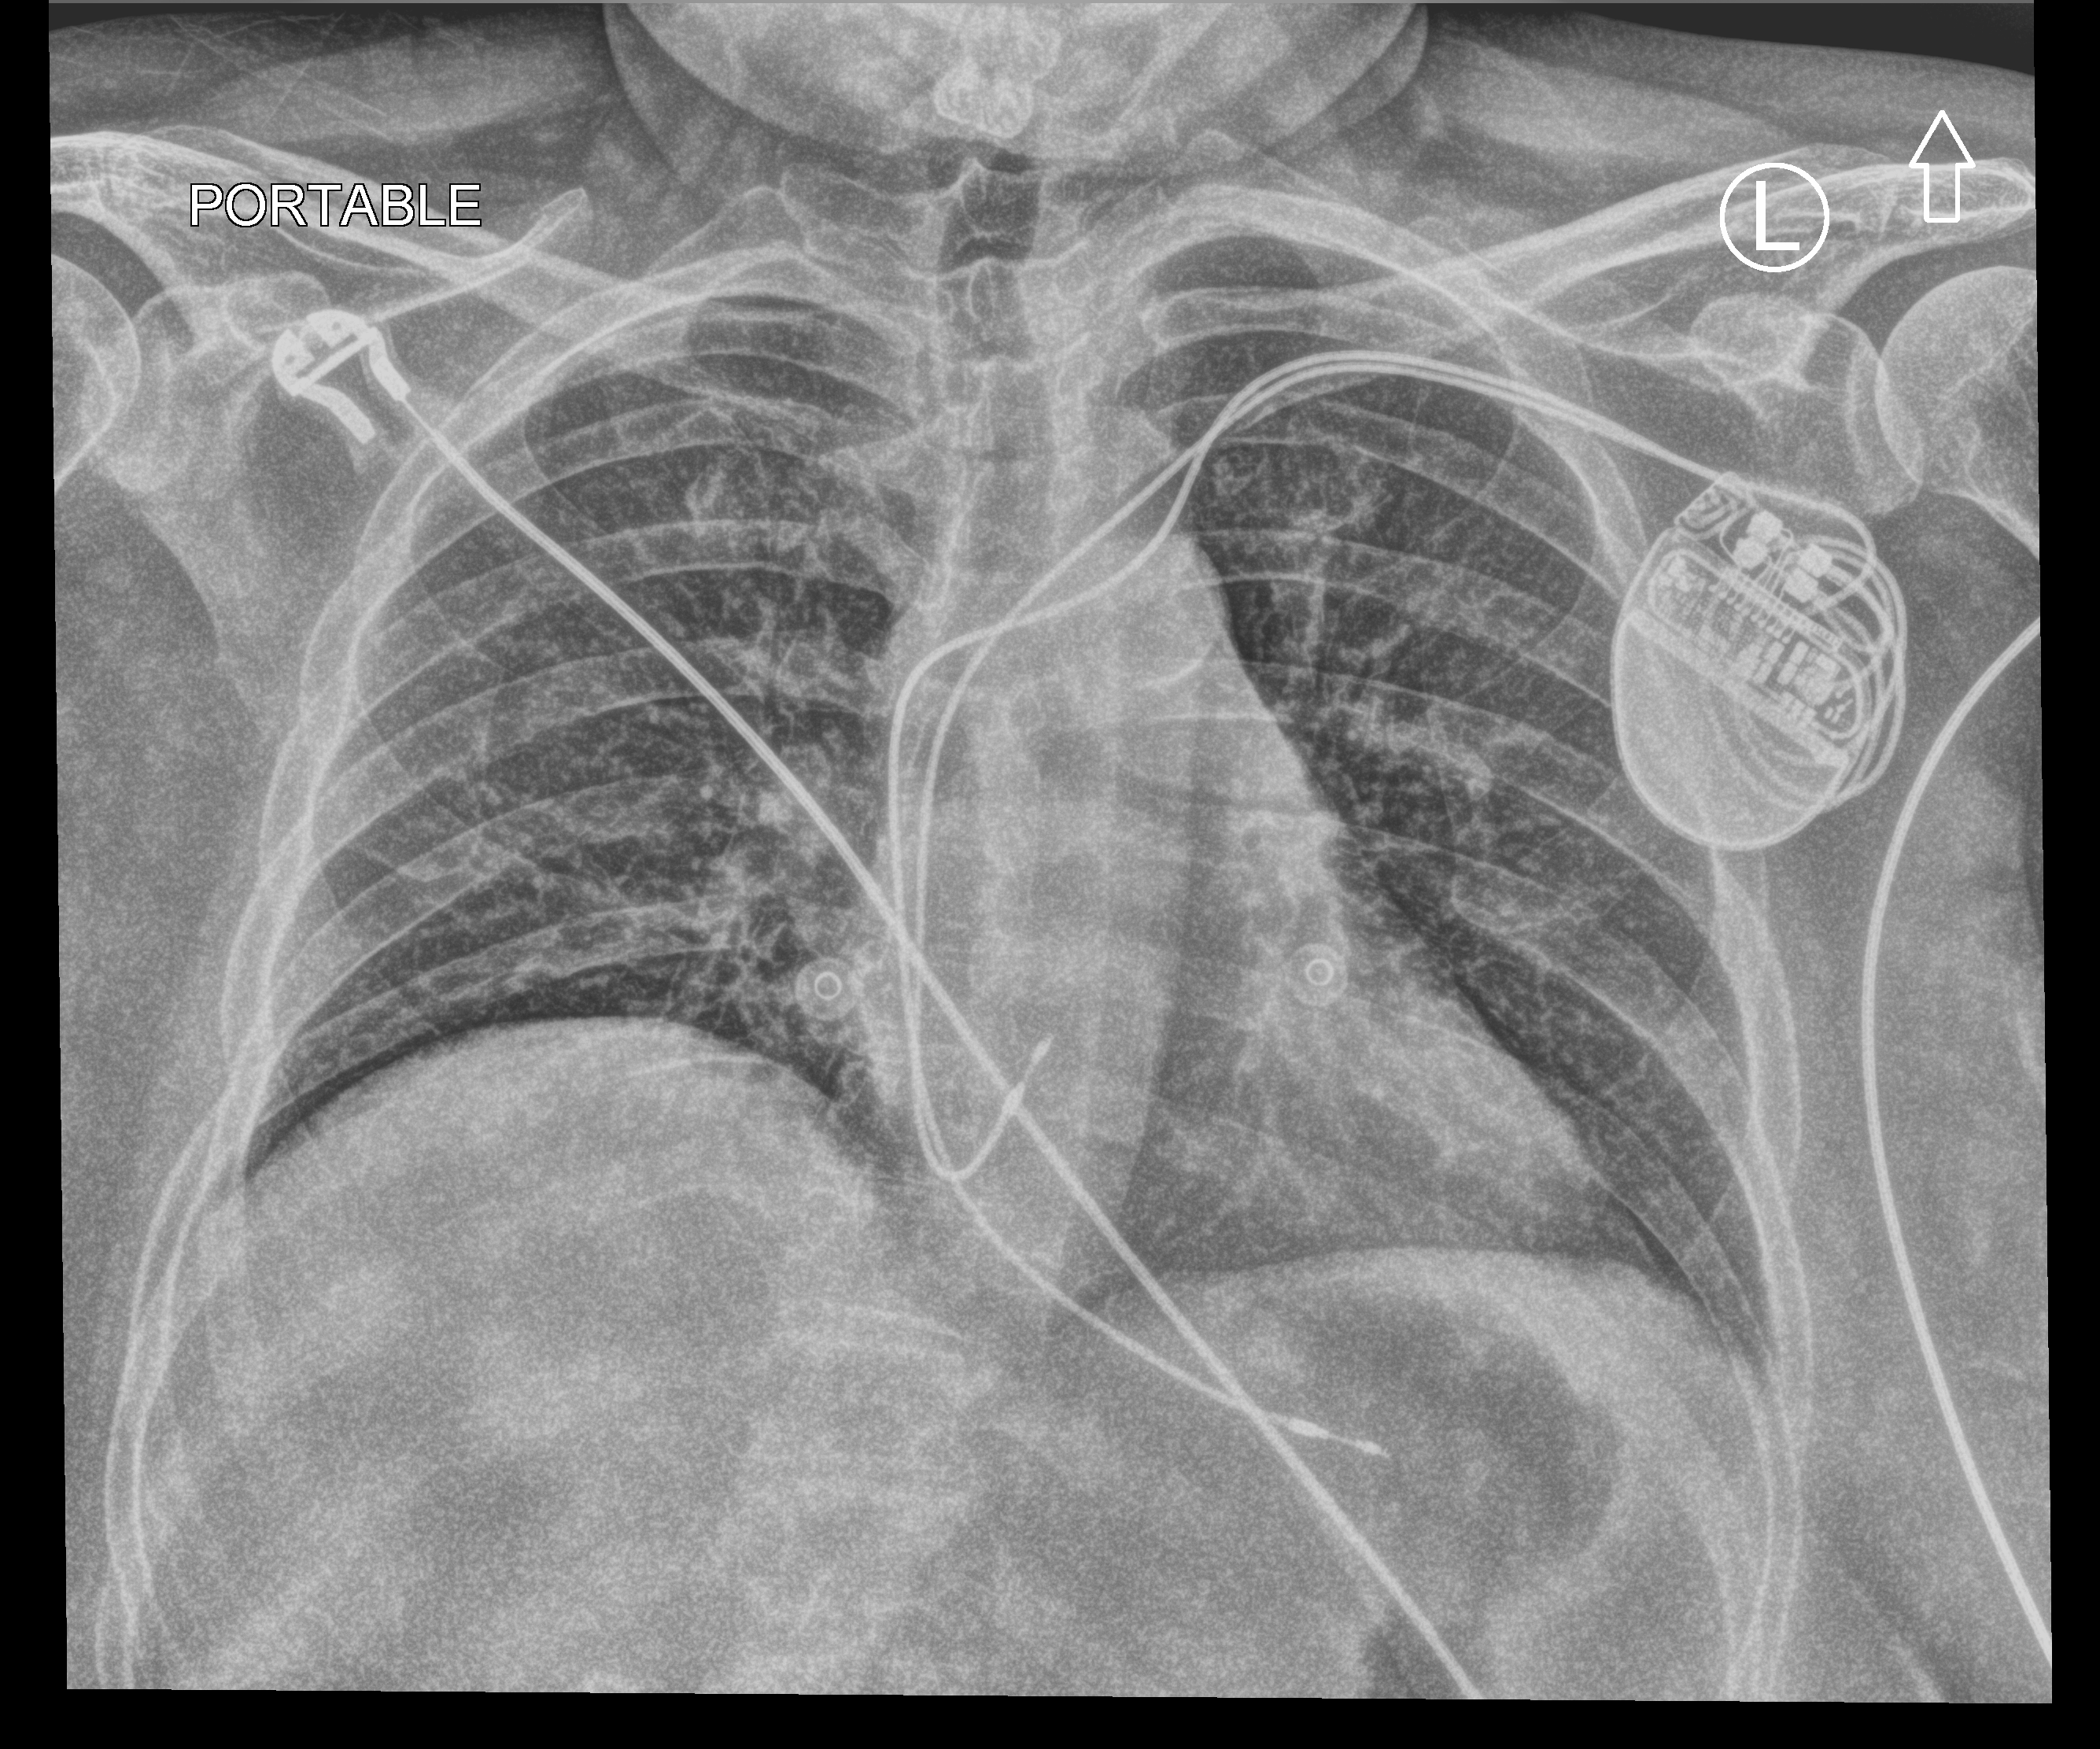
Portable chest radiograph. Patient hospitalised with COVID-19; female, aged 18–59 years.
Admission-level facts for this patient (not findings on this image; timing relative to this image not recorded): mechanically ventilated during this hospital stay: no.